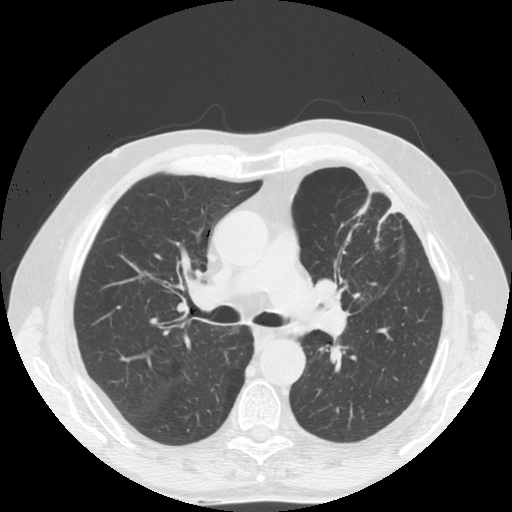
Low-dose screening chest CT, one axial slice. Position 109 of 170 along the scan axis. Reconstruction kernel STANDARD. 140 kVp. Lung window (W 1500 / L -600 HU). 512 × 512 image matrix.
Outlined on this slice (outlined manually by an expert reader):
- lesion 1 (tumor, upper lobe of left lung): bounding box (x1, y1, x2, y2) in pixels: (314, 279, 338, 299)